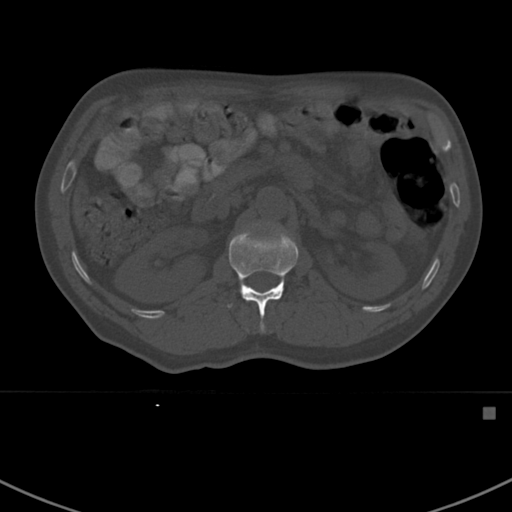
CT including the spine, one axial slice; slice 306 of 412 in the series (ordered by position); reconstruction kernel Br40s; bone window (W 1800 / L 400 HU); 512 × 512 image matrix, field of view 358 × 358 mm. Male patient, age 59 years. Case-level facts recorded for this patient, not image findings: primary cancer: prostate.
Outlined on this slice (semi-automatically segmented with operator editing):
- L1 vertebra: box from (x=228, y=228) to (x=298, y=333) px